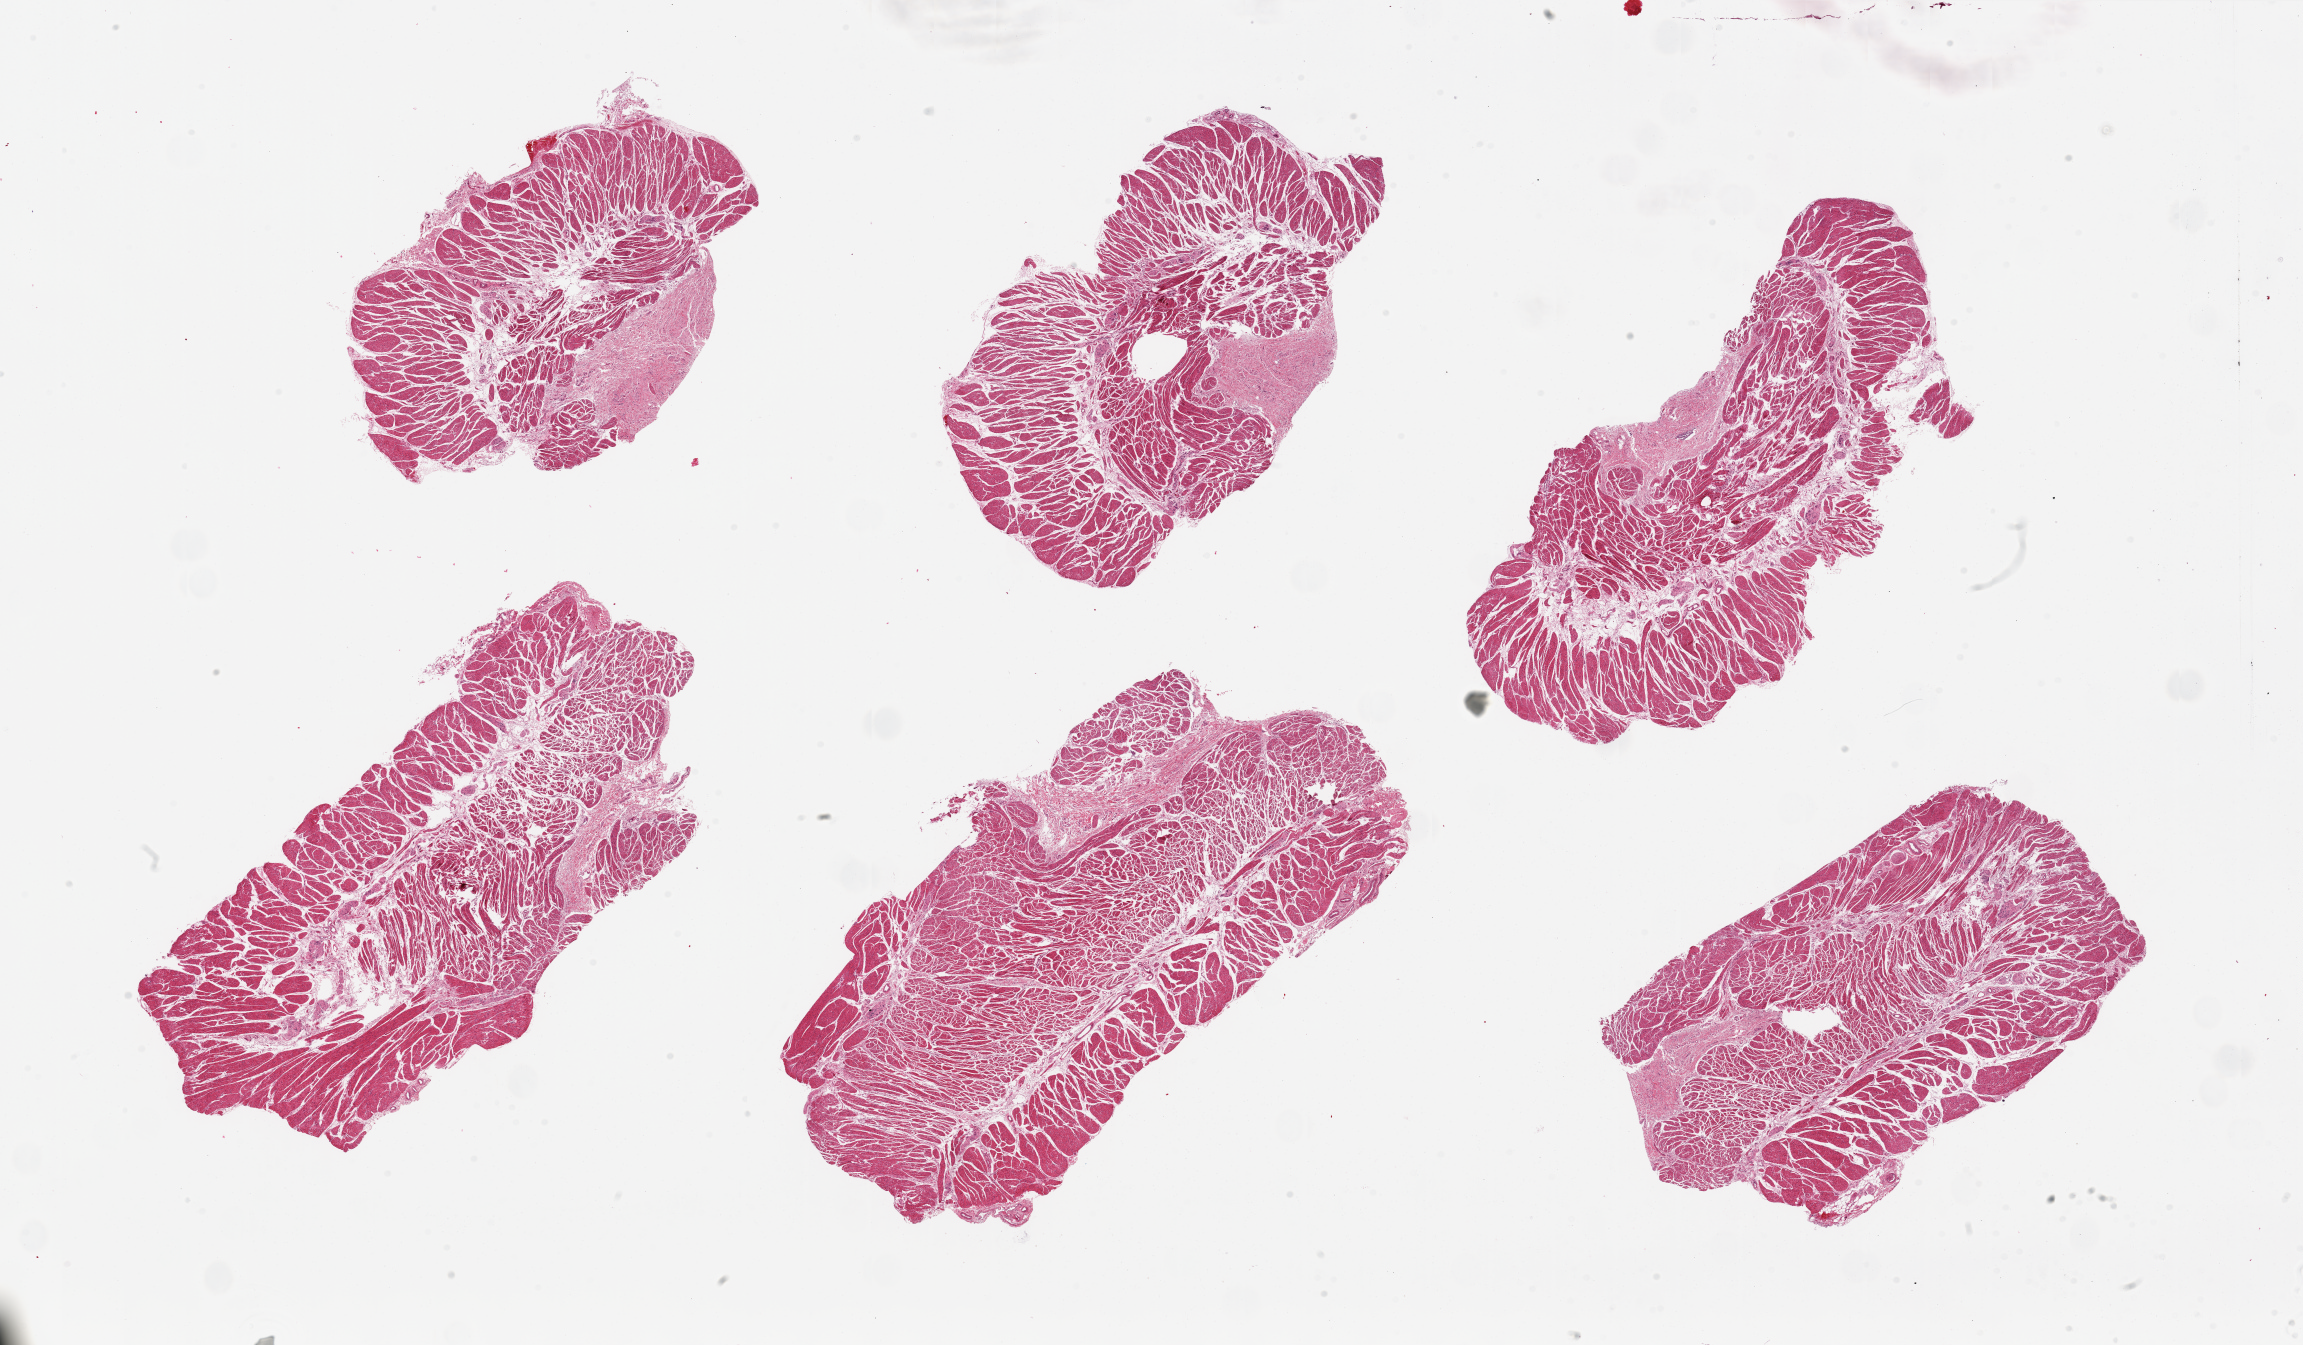
Whole-slide image, H&E stain, a low-resolution overview of the entire scanned area, about 36.4 x 21.3 mm (acquisition: 20x scan), PAXgene-fixed paraffin-embedded (PFPE) section, target tissue: esophageal muscle, donor tissue sample. Donor sex: female.
Review note (as recorded): 6 pieces, up to 11x5mm; all muscularis, good specimens.